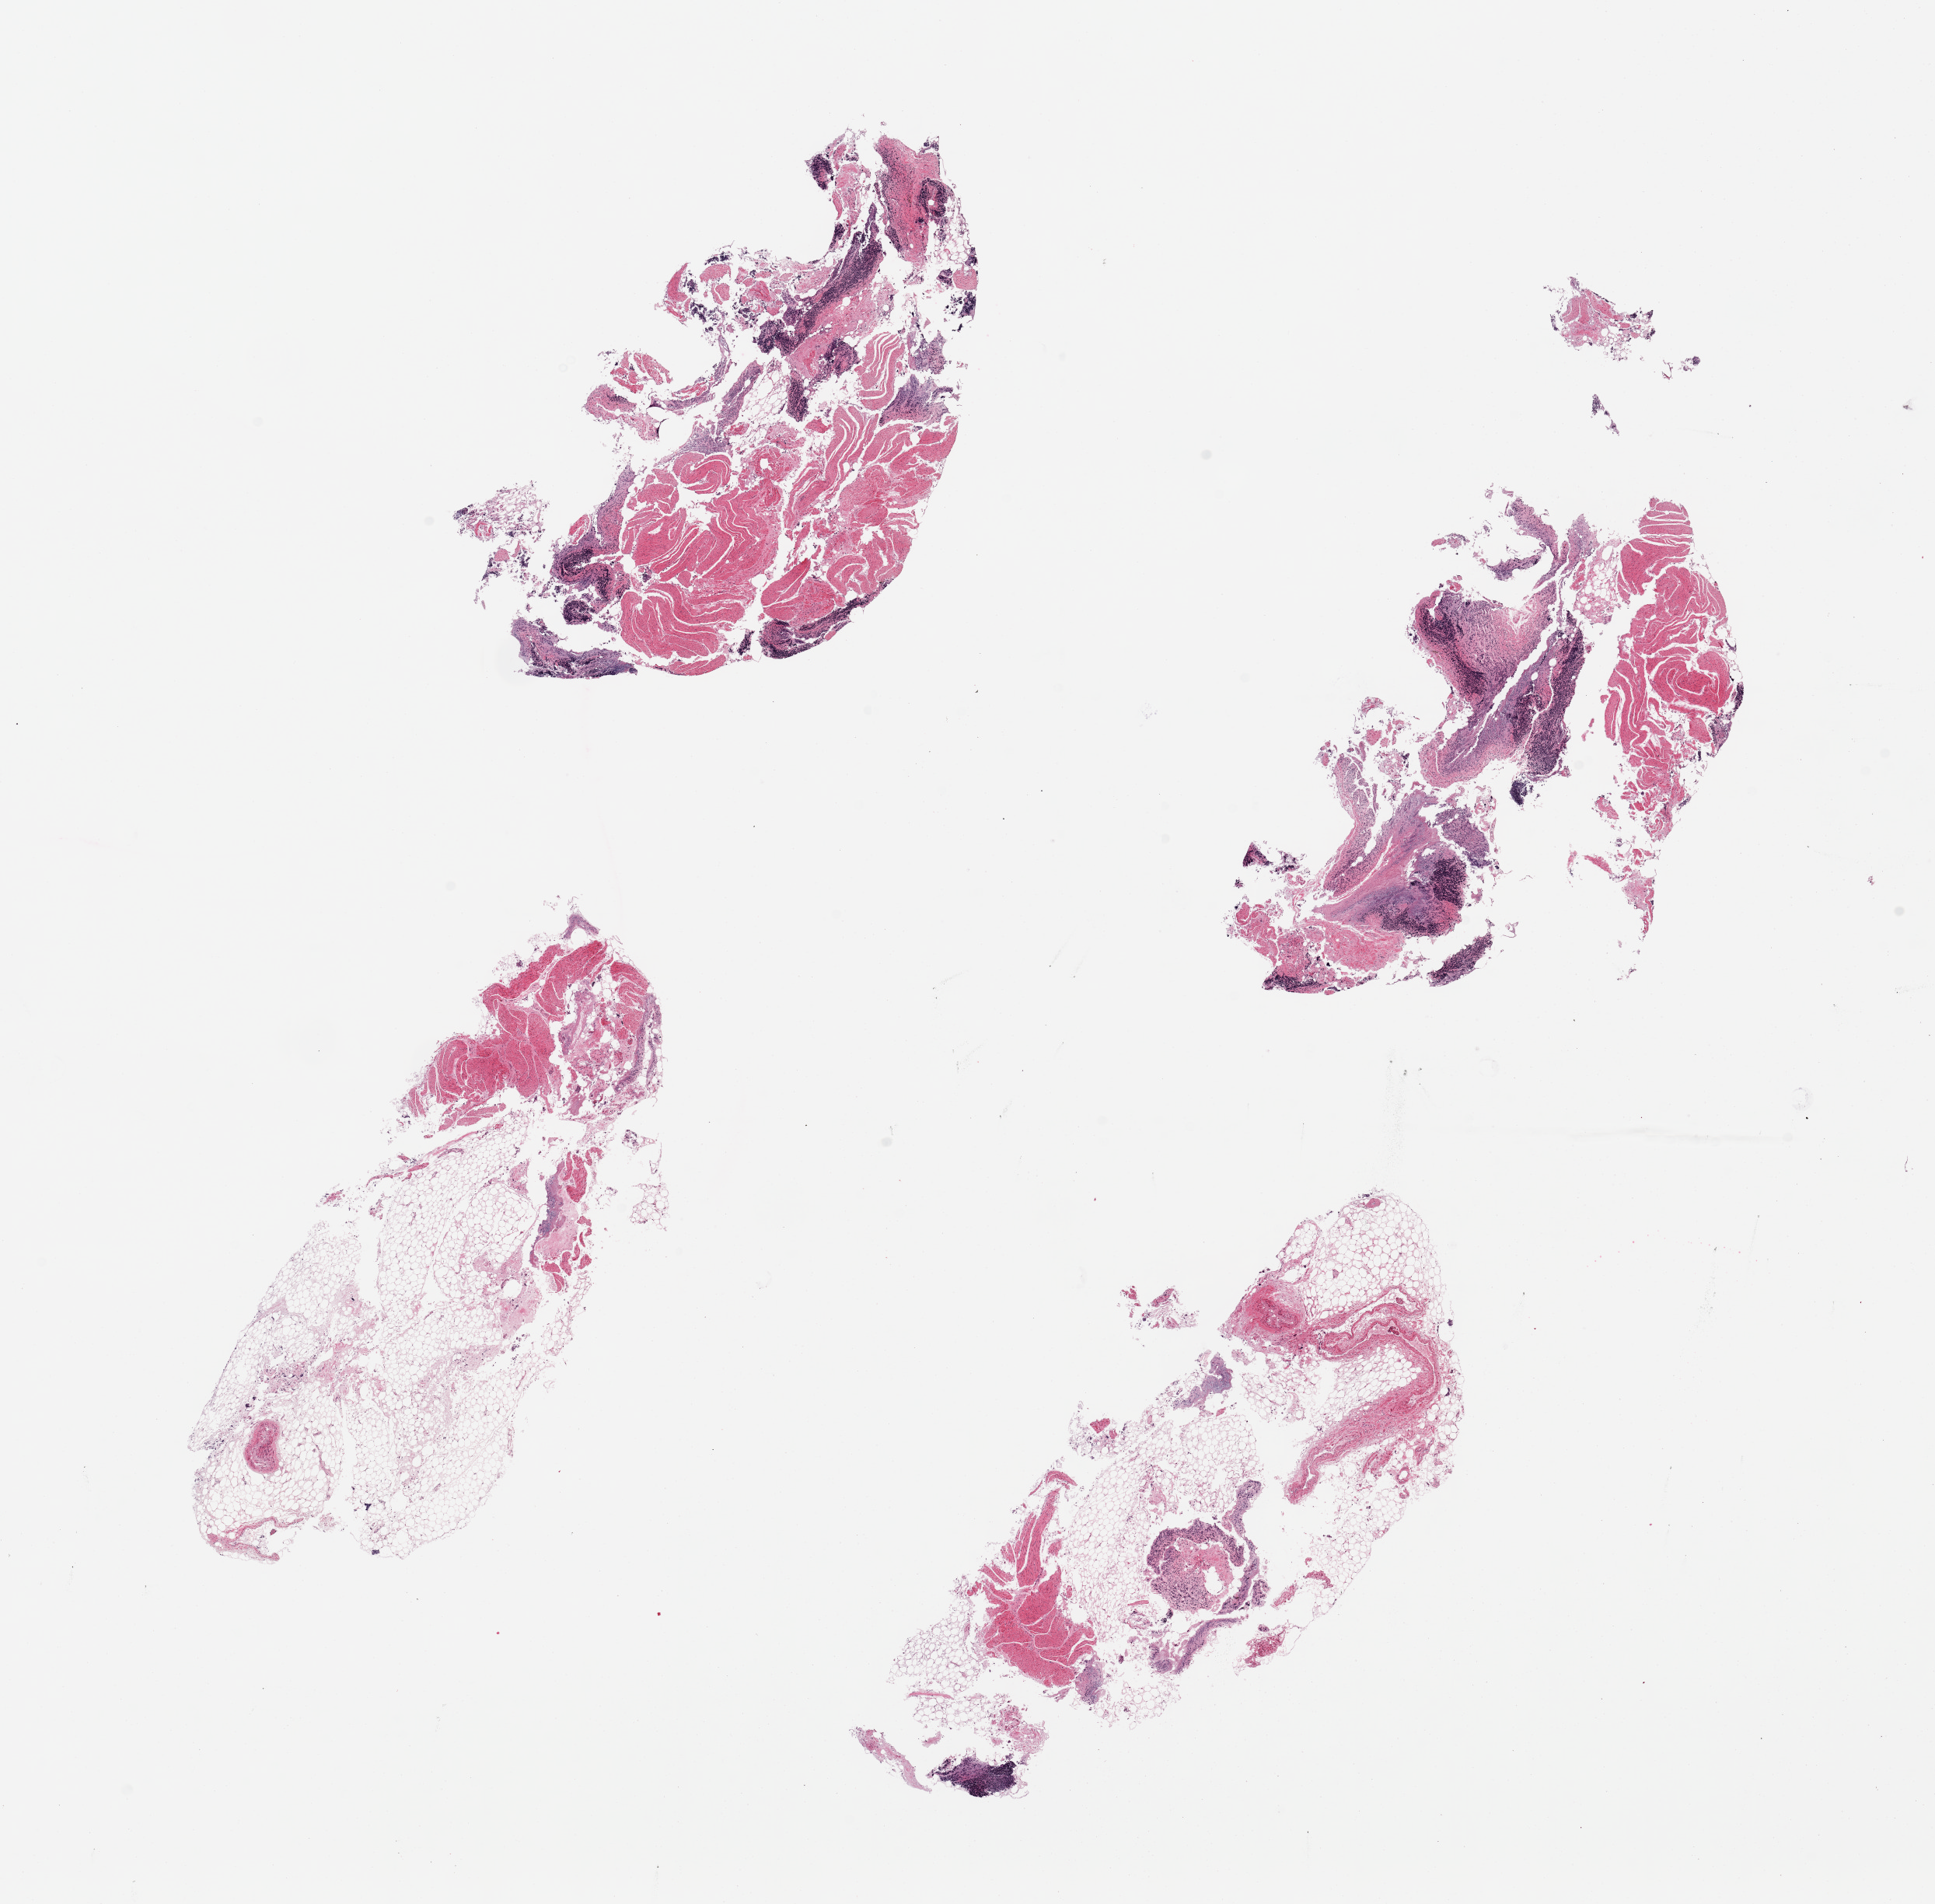
H&E whole-slide image — low-resolution overview of the scanned area, about 19.7 x 19.4 mm, PAXgene-fixed, paraffin-embedded tissue, section of ileum (target tissue), donor tissue sample. Male donor.
- reviewer comment on this tissue sample: 4 pieces; Several groups of lymphoid cells moderately autolyzed